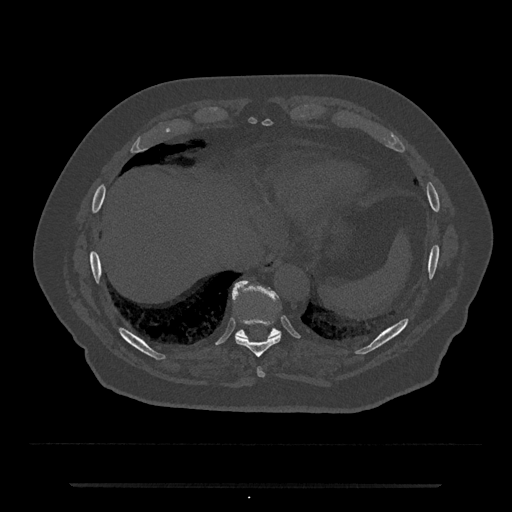
CT including the spine, one axial slice. Position 742 of 797 along the scan axis. Reconstruction kernel Br40s/3. Bone window (W 1800 / L 400 HU). 0.5 mm slice thickness. 512 × 512 image matrix. Patient: male, 80 years. Case-level facts recorded for this patient, not image findings: primary cancer: prostate; vertebrae with lytic lesions (as recorded): L1, T11.
Annotated regions visible in this slice (semi-automatically segmented with operator editing):
- T10 vertebra: bounding box [x1, y1, x2, y2] px = [232, 281, 281, 338]
- T8 vertebra: [257, 368, 265, 377]
- T9 vertebra: [235, 320, 281, 357]